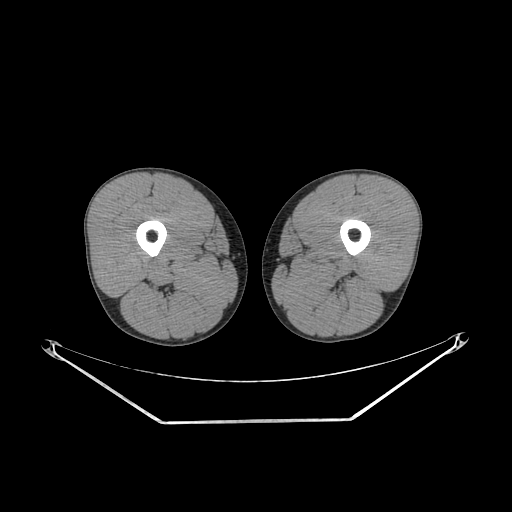
CT of an extremity soft-tissue mass (from a PET/CT study), one axial slice. Position 220 of 267 along the scan axis. Reconstruction kernel SOFT. Soft-tissue window (W 400 / L 40 HU). 3.75 mm slice thickness. 512 × 512 image matrix. Male patient. From the clinical record (not read from this slice): histological type: extraskeletal osteosarcoma; grade: high; site of the primary tumour: left adductur.
Annotated regions visible in this slice (expert contour drawn on MRI and transferred to this co-registered scan by the dataset authors):
- gross tumour volume (mass): box from (x=283, y=251) to (x=357, y=279) px